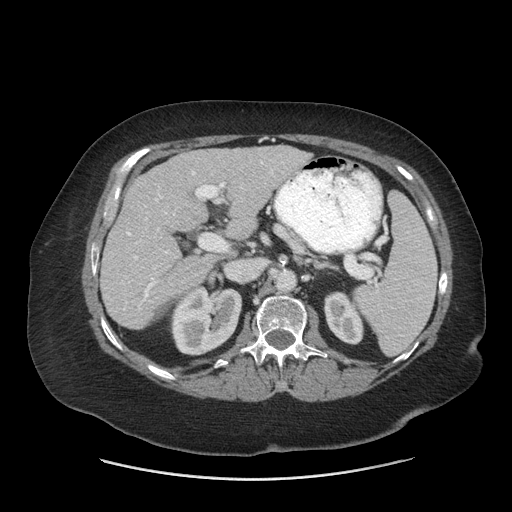
Contrast-enhanced abdominal CT (liver protocol), one axial slice; position 34 of 69 along the scan axis; soft-tissue window (W 400 / L 40 HU); 512 × 512 image matrix. From the clinical record (not read from this slice): diagnosis: hepatocellular carcinoma (patient treated with transarterial chemoembolisation; whether this scan precedes or follows treatment is not stated here); TNM stage (as recorded): Stage-IIIB; Child-Pugh class: A; tumour differentiation: moderately differentiated.
Structures marked on this image (semi-automatic segmentation, software-assisted and operator-edited):
- liver parenchyma outside the tumour (the mass and vessels are separate outlines, so this box may not span the whole liver): bounding box [x1, y1, x2, y2] px = [100, 146, 310, 328]
- liver vessels: [127, 161, 283, 308]